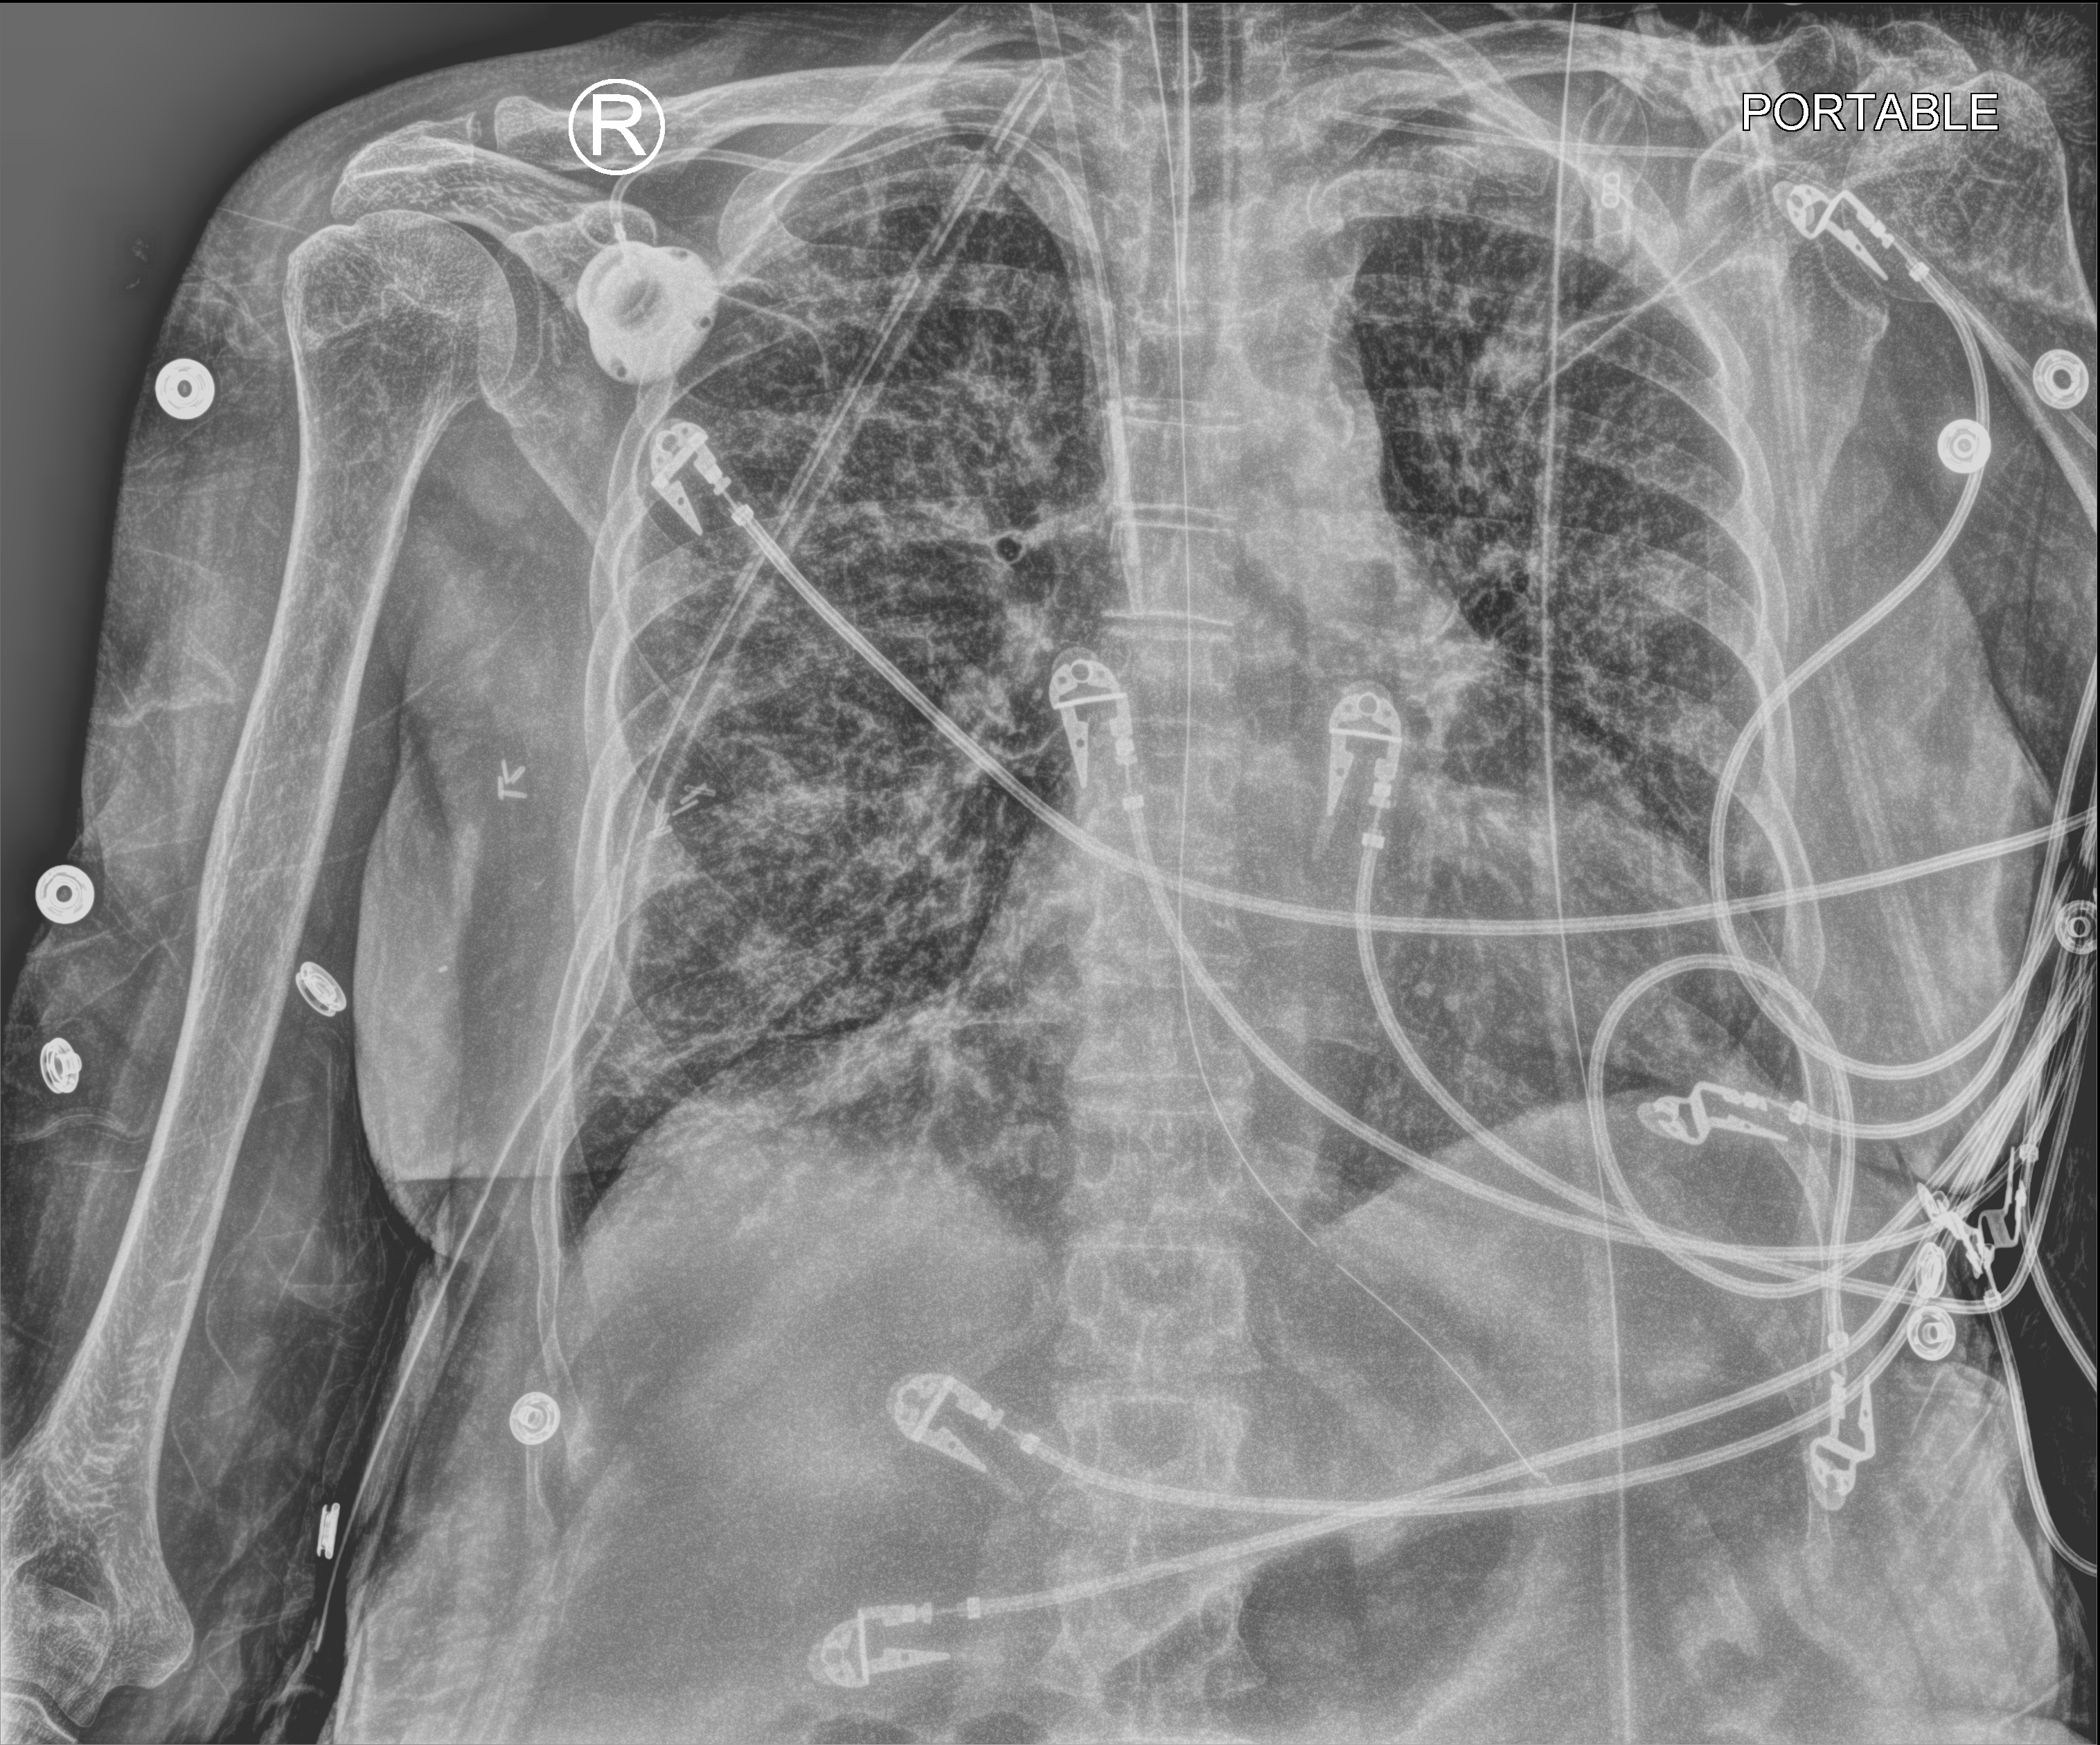
Portable chest radiograph; anteroposterior (AP) projection. Patient hospitalised with COVID-19; female, aged 60–74 years.
From the hospital-stay record, not from the radiograph (when in the stay this image was taken is not recorded):
- length of hospital stay: 43 days
- mechanically ventilated during this hospital stay: yes
- COPD (admission record): no